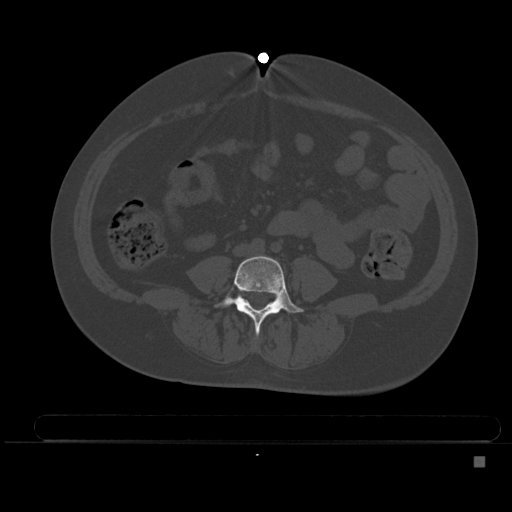
CT including the spine, one axial slice; slice 129 of 495 in the series (ordered by position); bone window (W 1800 / L 400 HU); 1.5 mm slice thickness; 512 × 512 image matrix. Patient: female, 33 years. From the clinical record (not read from this slice): primary cancer: breast.
Outlined on this slice (semi-automatic segmentation, software-assisted and operator-edited):
- L4 vertebra: bounding box (x1, y1, x2, y2) in pixels: (214, 255, 305, 333)